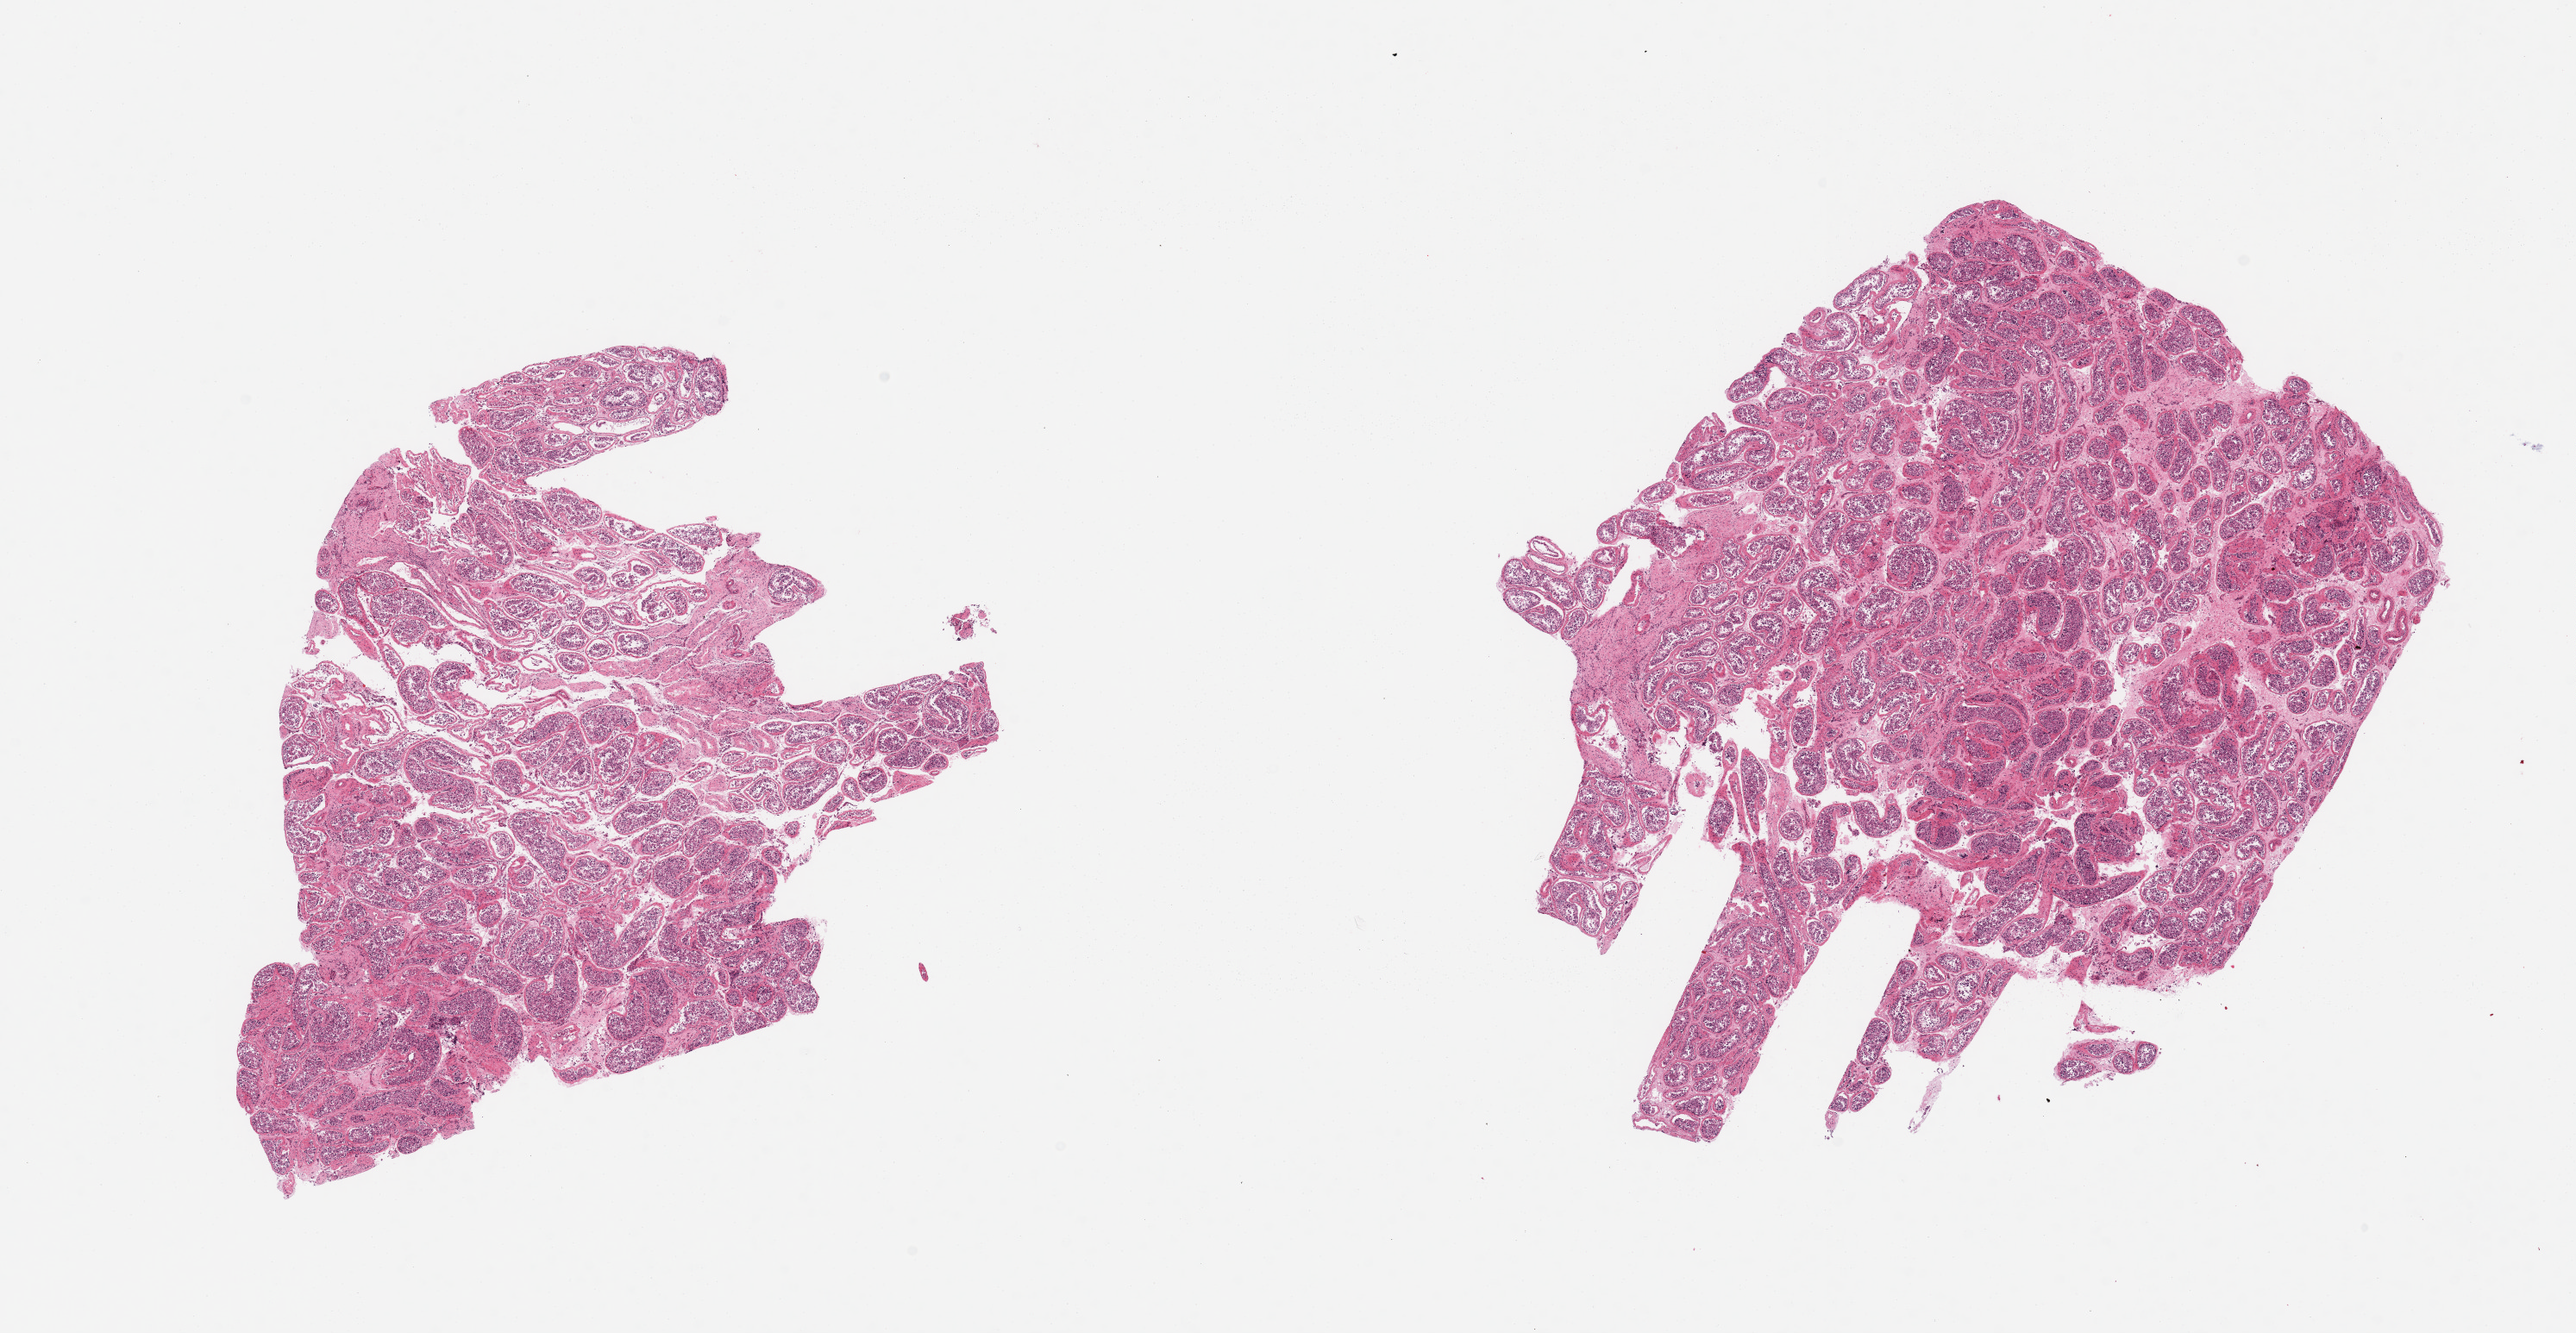
Digitized hematoxylin and eosin (H&E)-stained section — low-resolution overview of the scanned area, about 23.6 x 12.2 mm (slide scanned at 20x). PAXgene-fixed paraffin-embedded (PFPE) section. Sampled site (target tissue): testis. Tissue donor sample.
• pathologist's review note for this sample: 2 pieces; spermatogenesis is present, some tubules are hyalinized